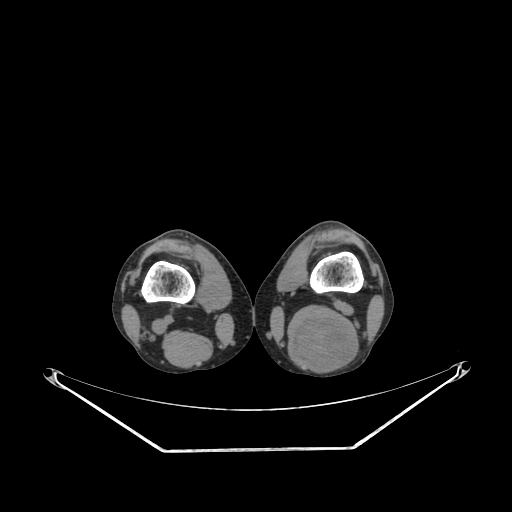
CT of an extremity soft-tissue mass (from a PET/CT study), one axial slice. Slice 190 of 267 in the series (ordered by position). 140 kVp. Soft-tissue window (W 400 / L 40 HU). 512 × 512 image matrix, field of view 500 × 500 mm. Male patient. Case-level facts recorded for this patient, not image findings: histological type: synovial sarcoma; site of the primary tumour: left poplietal fossa.
Outlined on this slice (expert contour drawn on MRI and transferred to this co-registered scan by the dataset authors):
- gross tumour volume (mass): bounding box <288,315,359,371> (left, top, right, bottom; pixels)